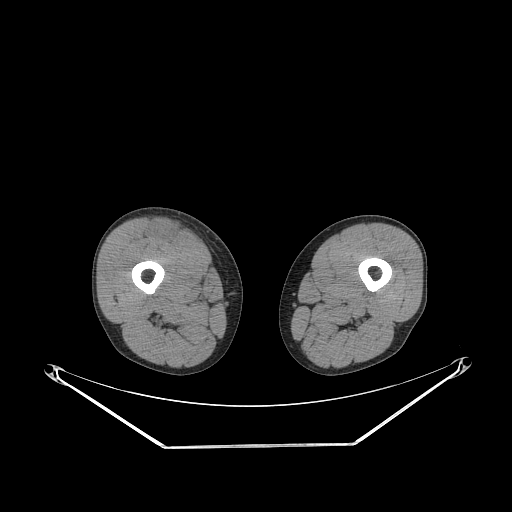
CT of an extremity soft-tissue mass (from a PET/CT study), one axial slice; position 241 of 311 along the scan axis; soft-tissue window (W 400 / L 40 HU); 3.75 mm slice thickness; 512 × 512 image matrix, field of view 500 × 500 mm. Male patient. Case-level facts recorded for this patient, not image findings: histological type: pleiomorphic leiomyosarcoma; grade: intermediate; site of the primary tumour: right thigh.
Annotated regions visible in this slice (expert contour drawn on MRI and transferred to this co-registered scan by the dataset authors):
- gross tumour volume including surrounding oedema: bounding box [x1, y1, x2, y2] px = [151, 221, 182, 243]